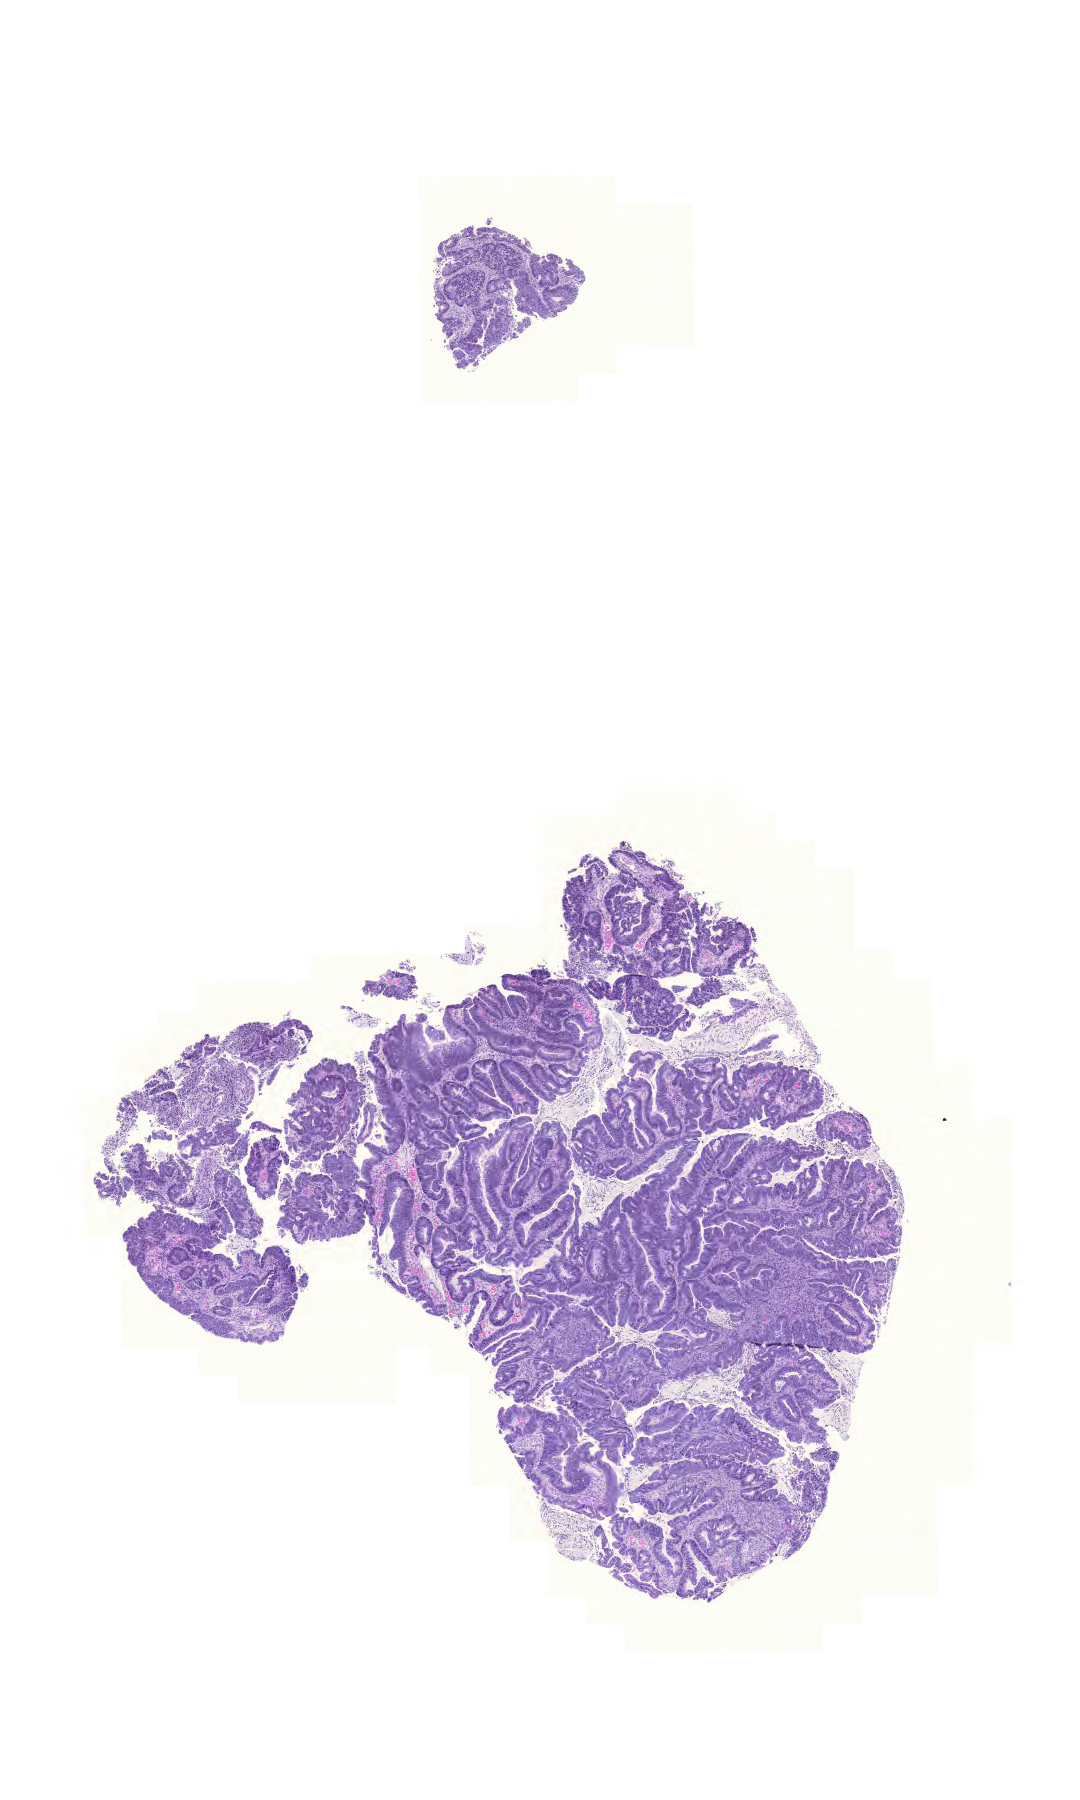
Hematoxylin and eosin (H&E) stained whole-slide image, shown as a low-resolution overview of the whole scanned area (about 8.0 x 13.4 mm, acquisition: 20x scan); formalin-fixed paraffin-embedded (FFPE) diagnostic section; sample: primary tumour, colon. Patient: male, age at initial diagnosis 65 years.
- histologic diagnosis: Adenocarcinoma, NOS
- lymph nodes positive (case pathology): 0 of 15 examined